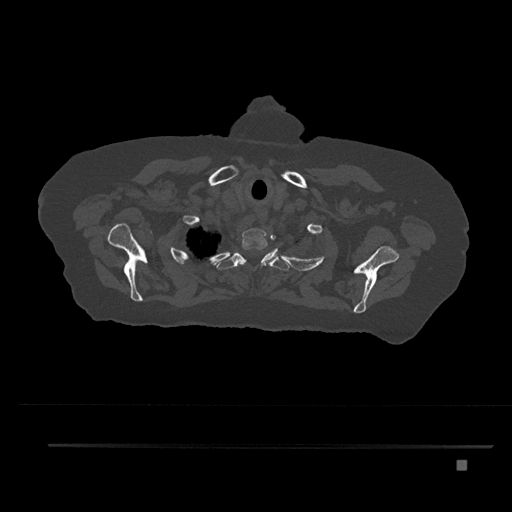
CT including the spine, one axial slice. Slice 682 of 797 in the series (ordered by position). Reconstruction kernel Br40s/3. 120 kVp. Bone window (W 1800 / L 400 HU). 512 × 512 image matrix, field of view 437 × 437 mm. Female patient, age 76 years. From the clinical record (not read from this slice): primary cancer: lung.
Annotated regions visible in this slice (semi-automatic segmentation, software-assisted and operator-edited):
- T1 vertebra: bounding box (x1, y1, x2, y2) in pixels: (238, 228, 278, 265)
- T2 vertebra: (216, 249, 290, 271)